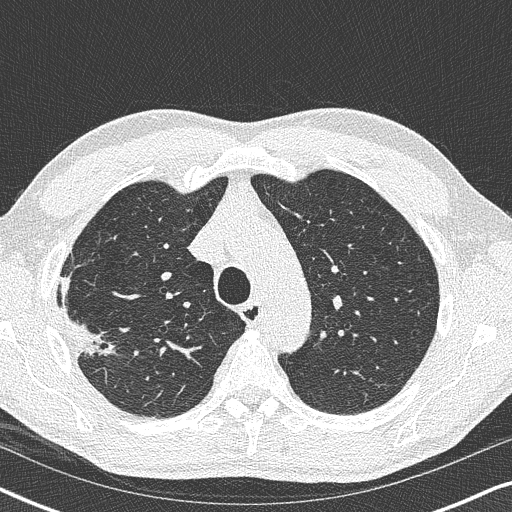
Low-dose screening chest CT, one axial slice; slice 275 of 356 in the series (ordered by position); reconstruction kernel B50f; 120 kVp; lung window (W 1500 / L -600 HU); 1 mm slice thickness; 512 × 512 image matrix, field of view 330 × 330 mm.
Outlined on this slice (outlined manually by an expert reader):
- lesion 1 (tumor, upper lobe of right lung): bounding box <64,306,117,356> (left, top, right, bottom; pixels)